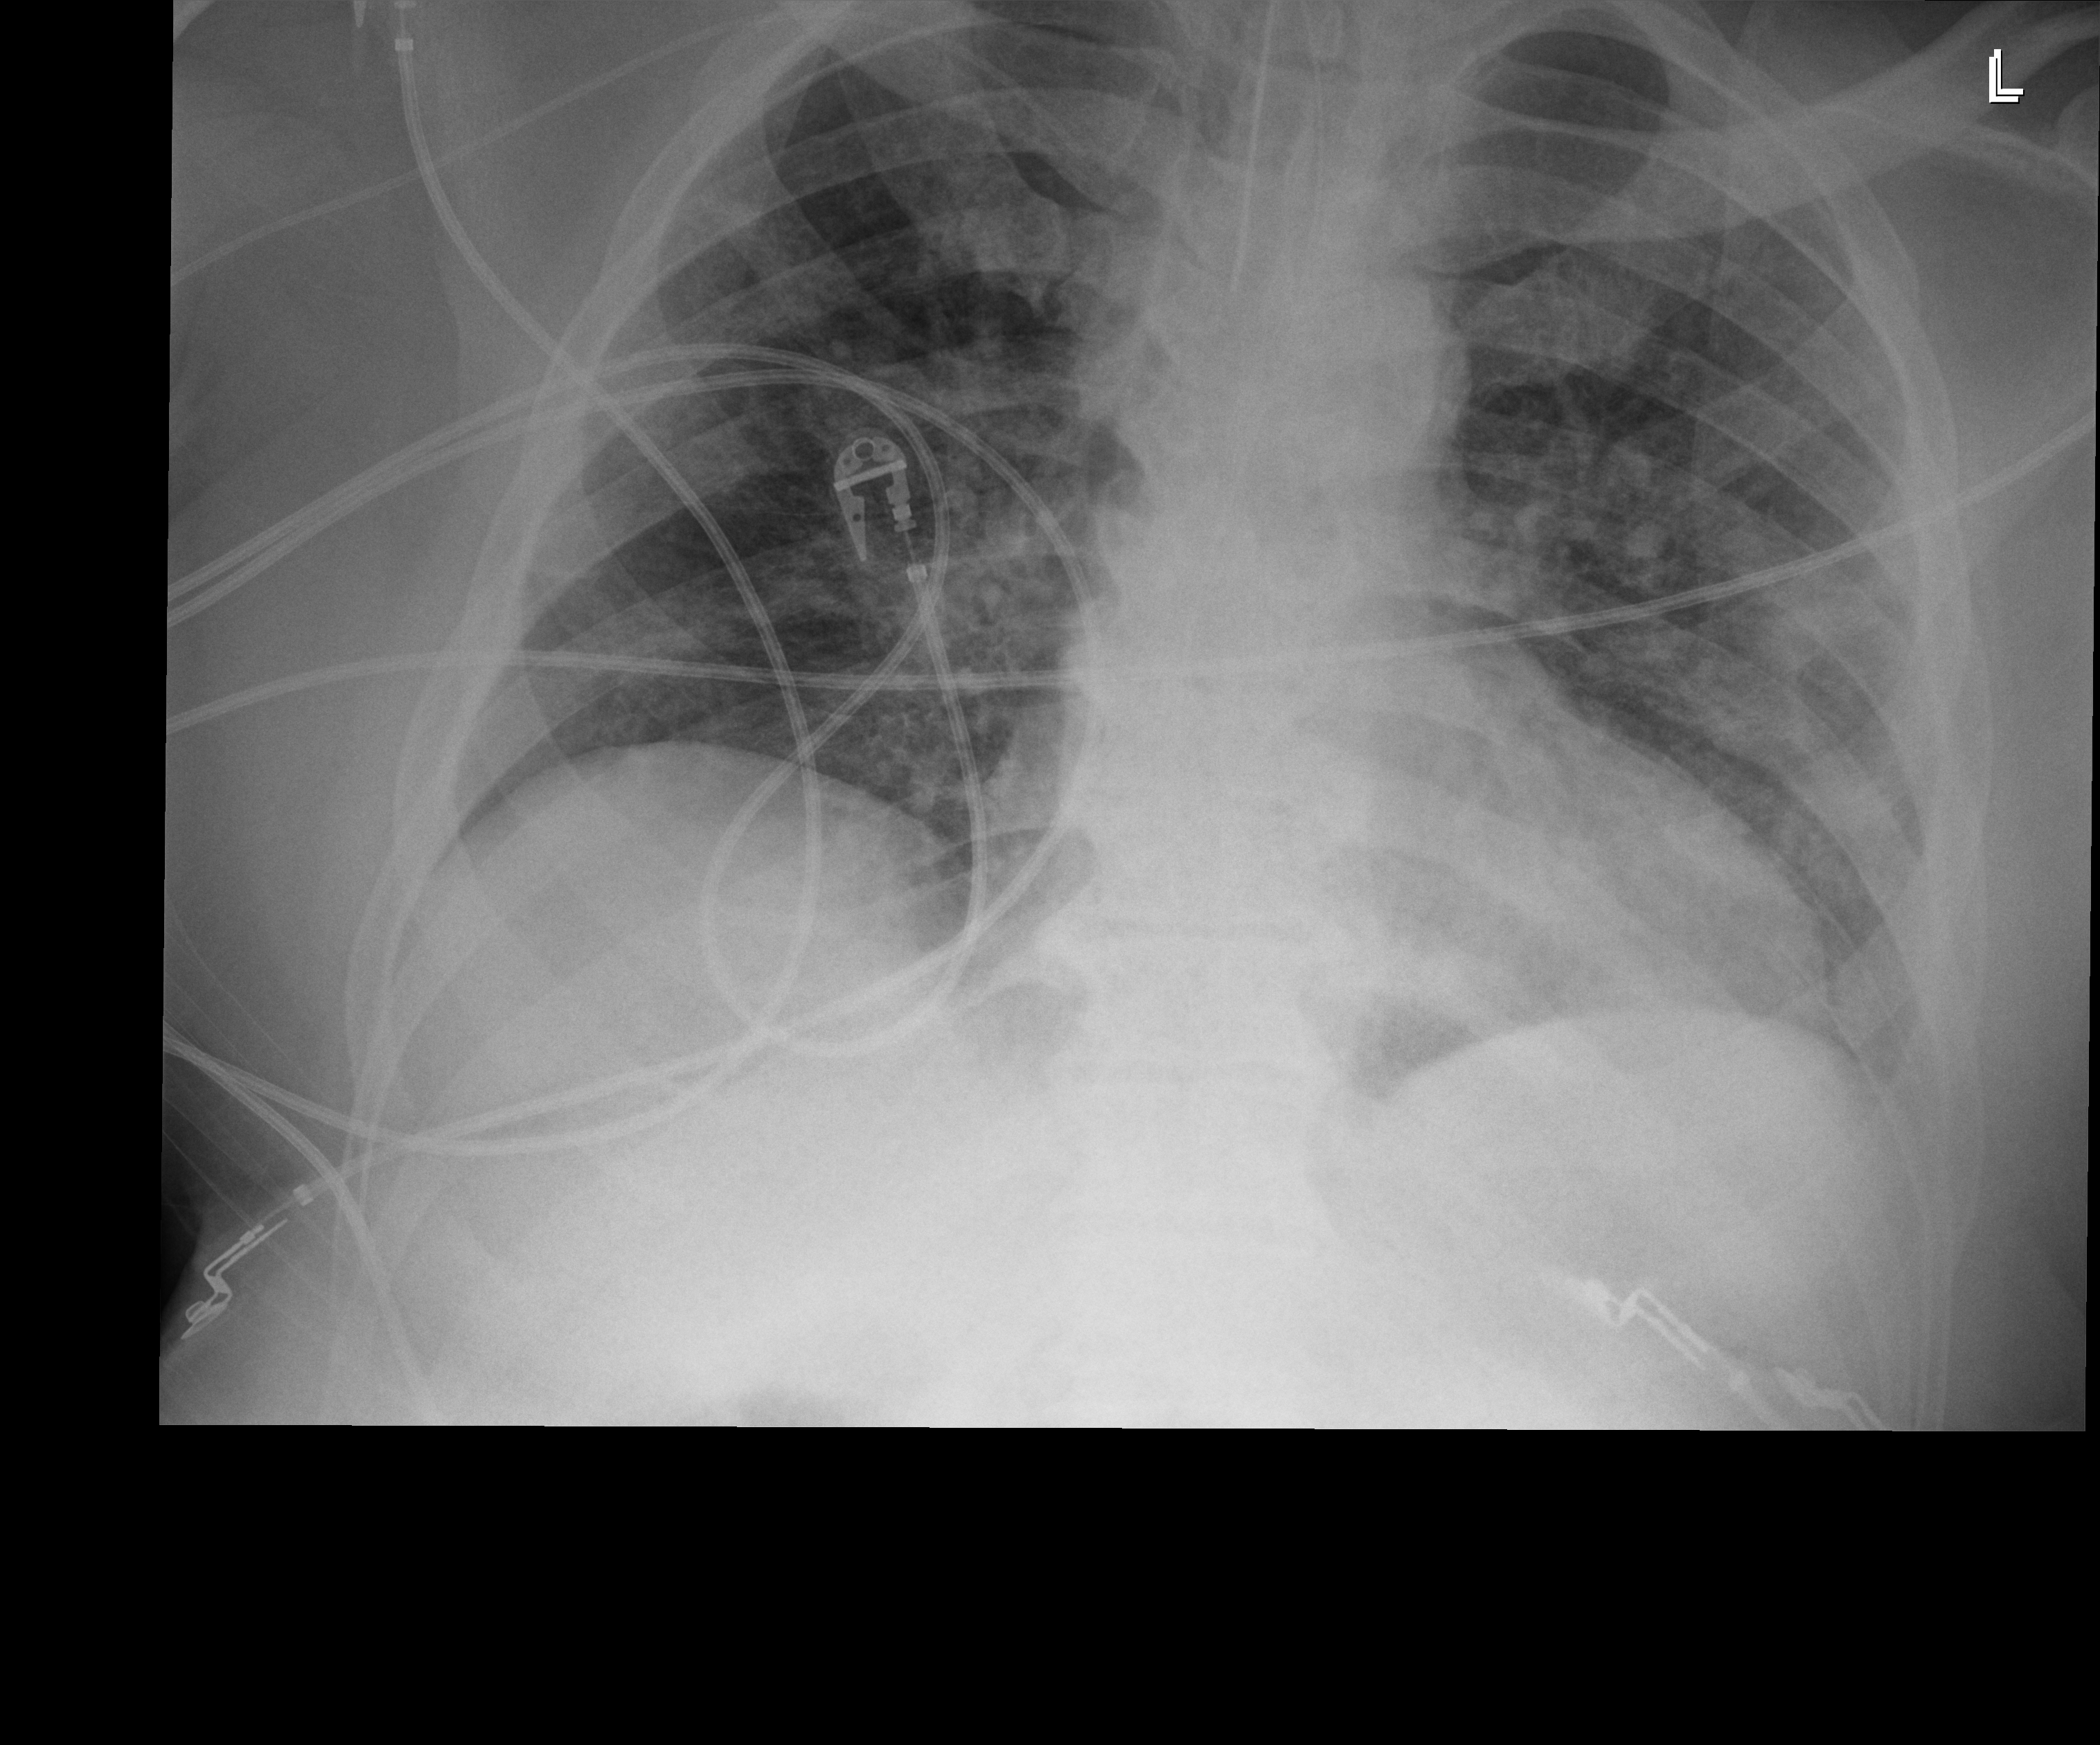
Chest radiograph, anteroposterior (AP) projection. Male patient hospitalised with COVID-19, age 18–59 years.
Admission-level facts for this patient (not findings on this image; timing relative to this image not recorded): mechanically ventilated during this hospital stay: yes; diabetes (admission record): no.